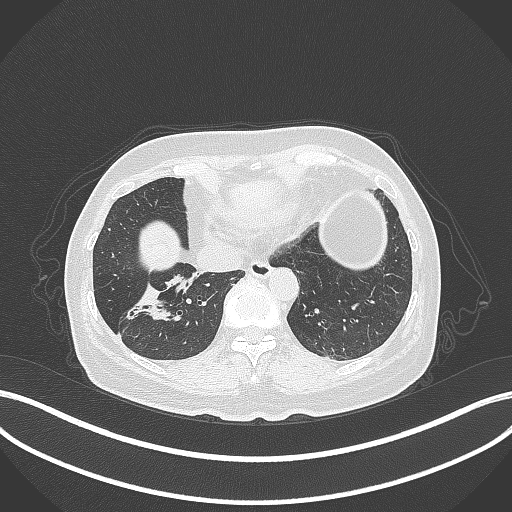
Chest CT, one axial slice. Slice 106 of 429 in the series (ordered by position). 120 kVp. Lung window (W 1500 / L -600 HU). 1 mm slice thickness. 512 × 512 image matrix, field of view 400 × 400 mm. Female patient, age 67 years. Case-level facts recorded for this patient, not image findings: clinical TNM (as recorded): T1c N1 M0.
Annotated regions visible in this slice (rectangle marked by the reading radiologist):
- lung tumour (recorded histology: adenocarcinoma): bounding box <122,273,189,327> (left, top, right, bottom; pixels)